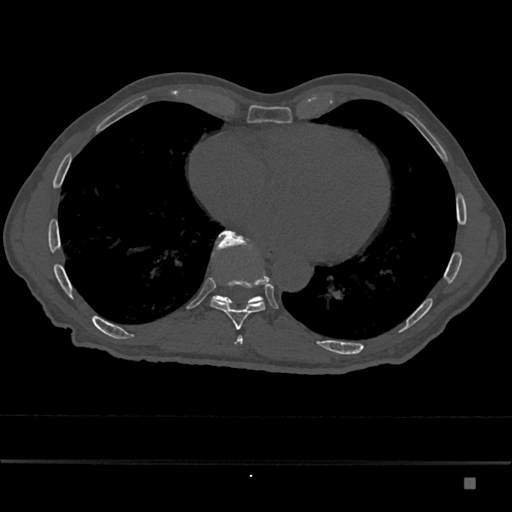
CT including the spine, one axial slice; slice 787 of 797 in the series (ordered by position); 120 kVp; bone window (W 1800 / L 400 HU); 512 × 512 image matrix, field of view 390 × 390 mm. Patient: male, 72 years. From the clinical record (not read from this slice): primary cancer: prostate.
Annotated regions visible in this slice (semi-automatic segmentation, software-assisted and operator-edited):
- T10 vertebra: box from (x=212, y=231) to (x=263, y=304) px
- T9 vertebra: (x=210, y=230)–(x=269, y=330)